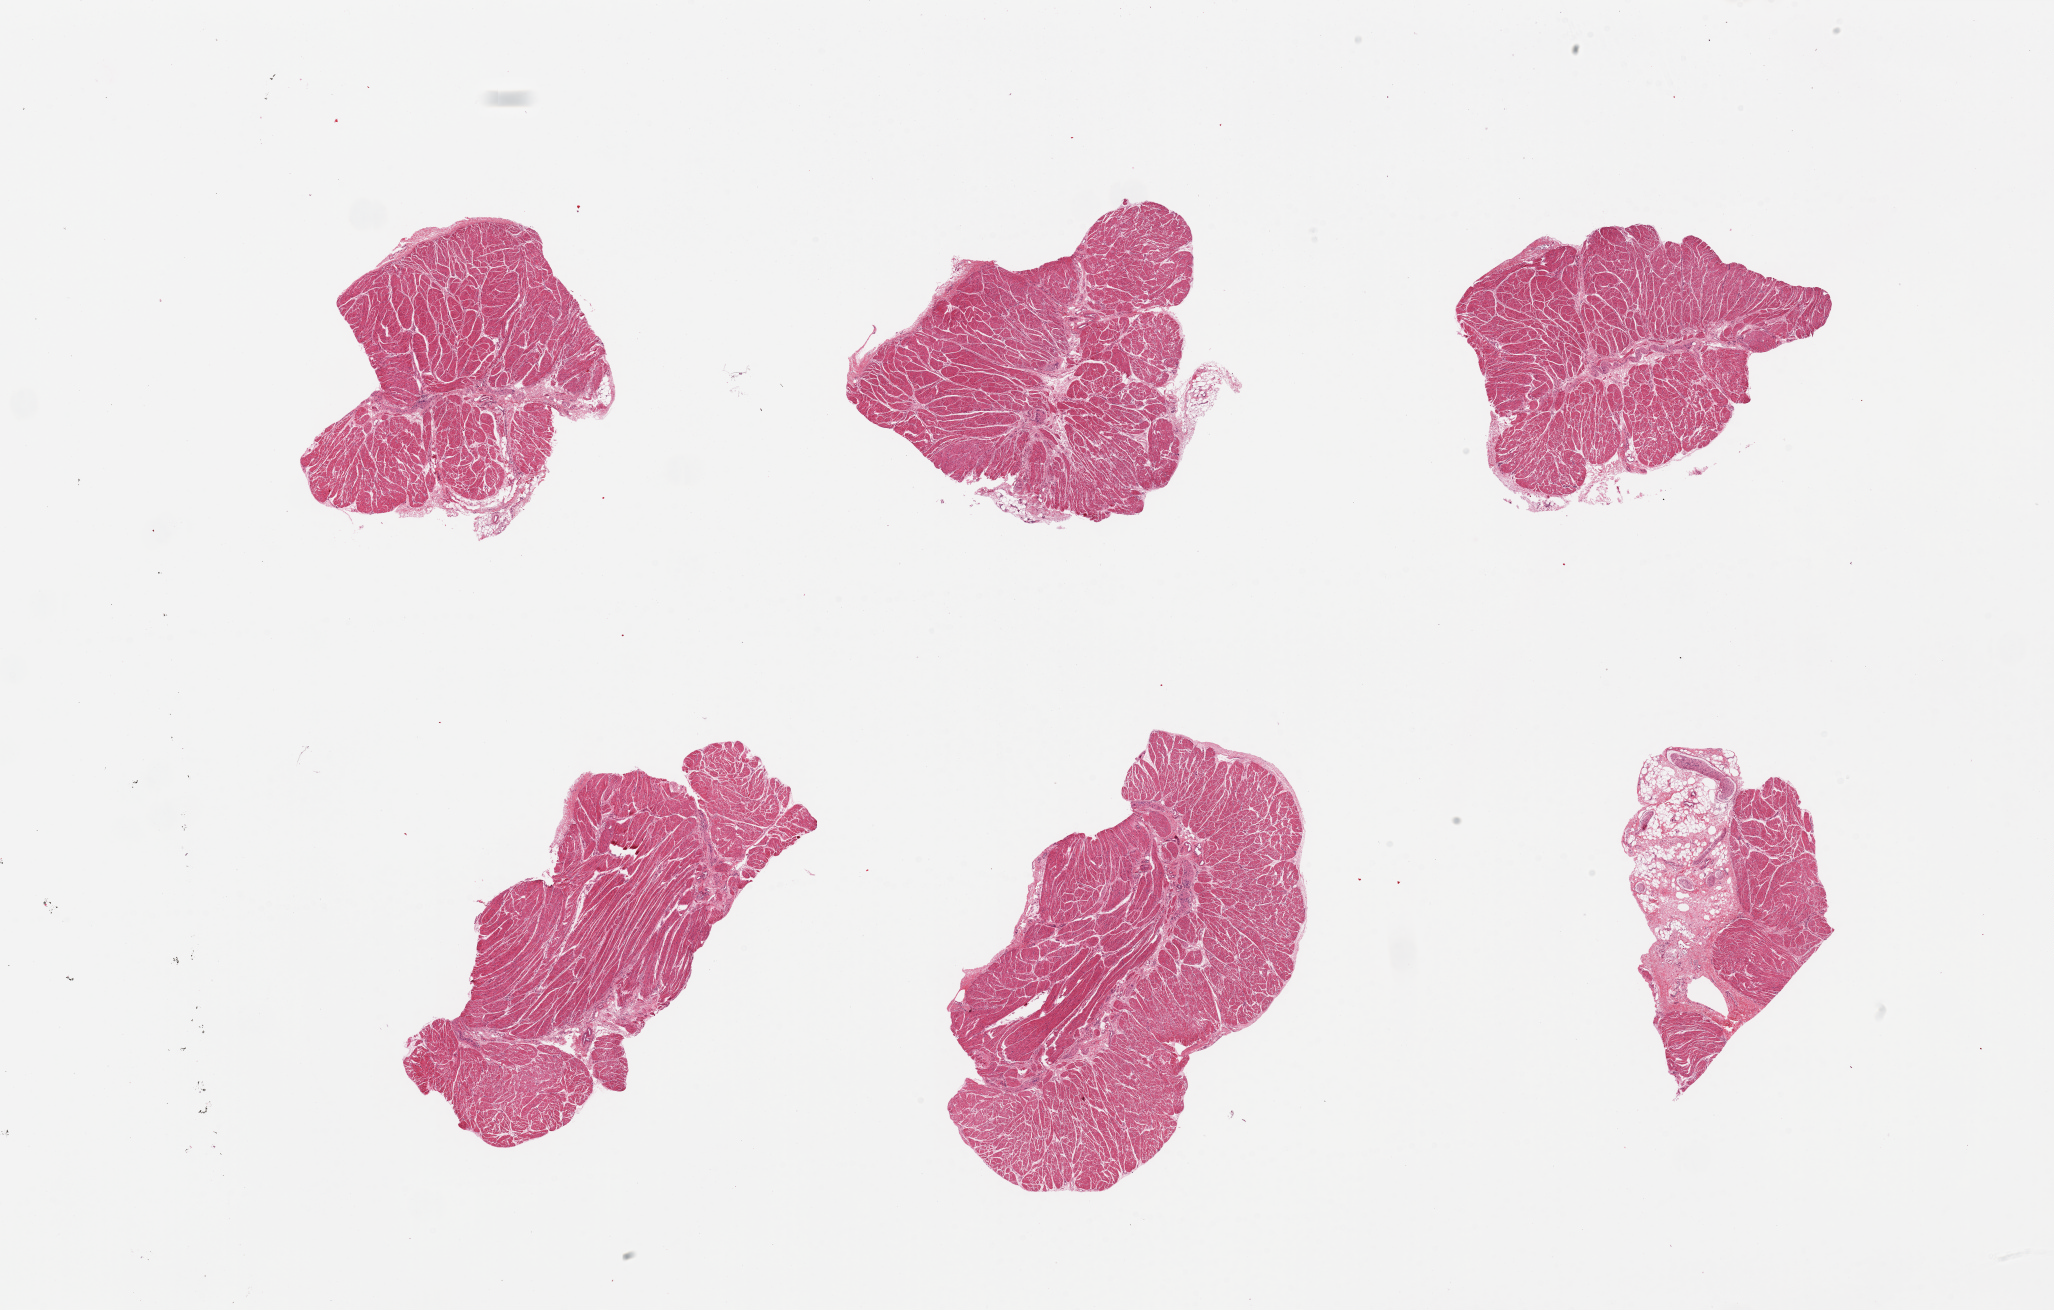
Whole-slide image, hematoxylin and eosin (H&E) stain — shown as a low-resolution overview of the whole scanned area (about 32.5 x 20.7 mm), PAXgene-fixed, paraffin-embedded tissue, sampled site (target tissue): esophageal muscle, tissue donor sample. Donor sex: male.
- reviewer comment on this tissue sample: 6 pieces, 1 with 50% fibroadipose